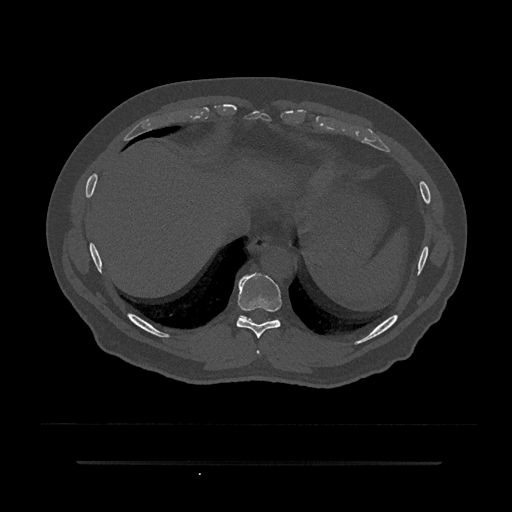
CT including the spine, one axial slice. Position 368 of 797 along the scan axis. Reconstruction kernel Br40s/3. 120 kVp. Bone window (W 1800 / L 400 HU). 512 × 512 image matrix. Patient: male, 59 years. Case-level facts recorded for this patient, not image findings: primary cancer: bile ducts.
Outlined on this slice (semi-automatically segmented with operator editing):
- T8 vertebra: bounding box (x1, y1, x2, y2) in pixels: (257, 351, 260, 355)
- T9 vertebra: (236, 273, 282, 338)